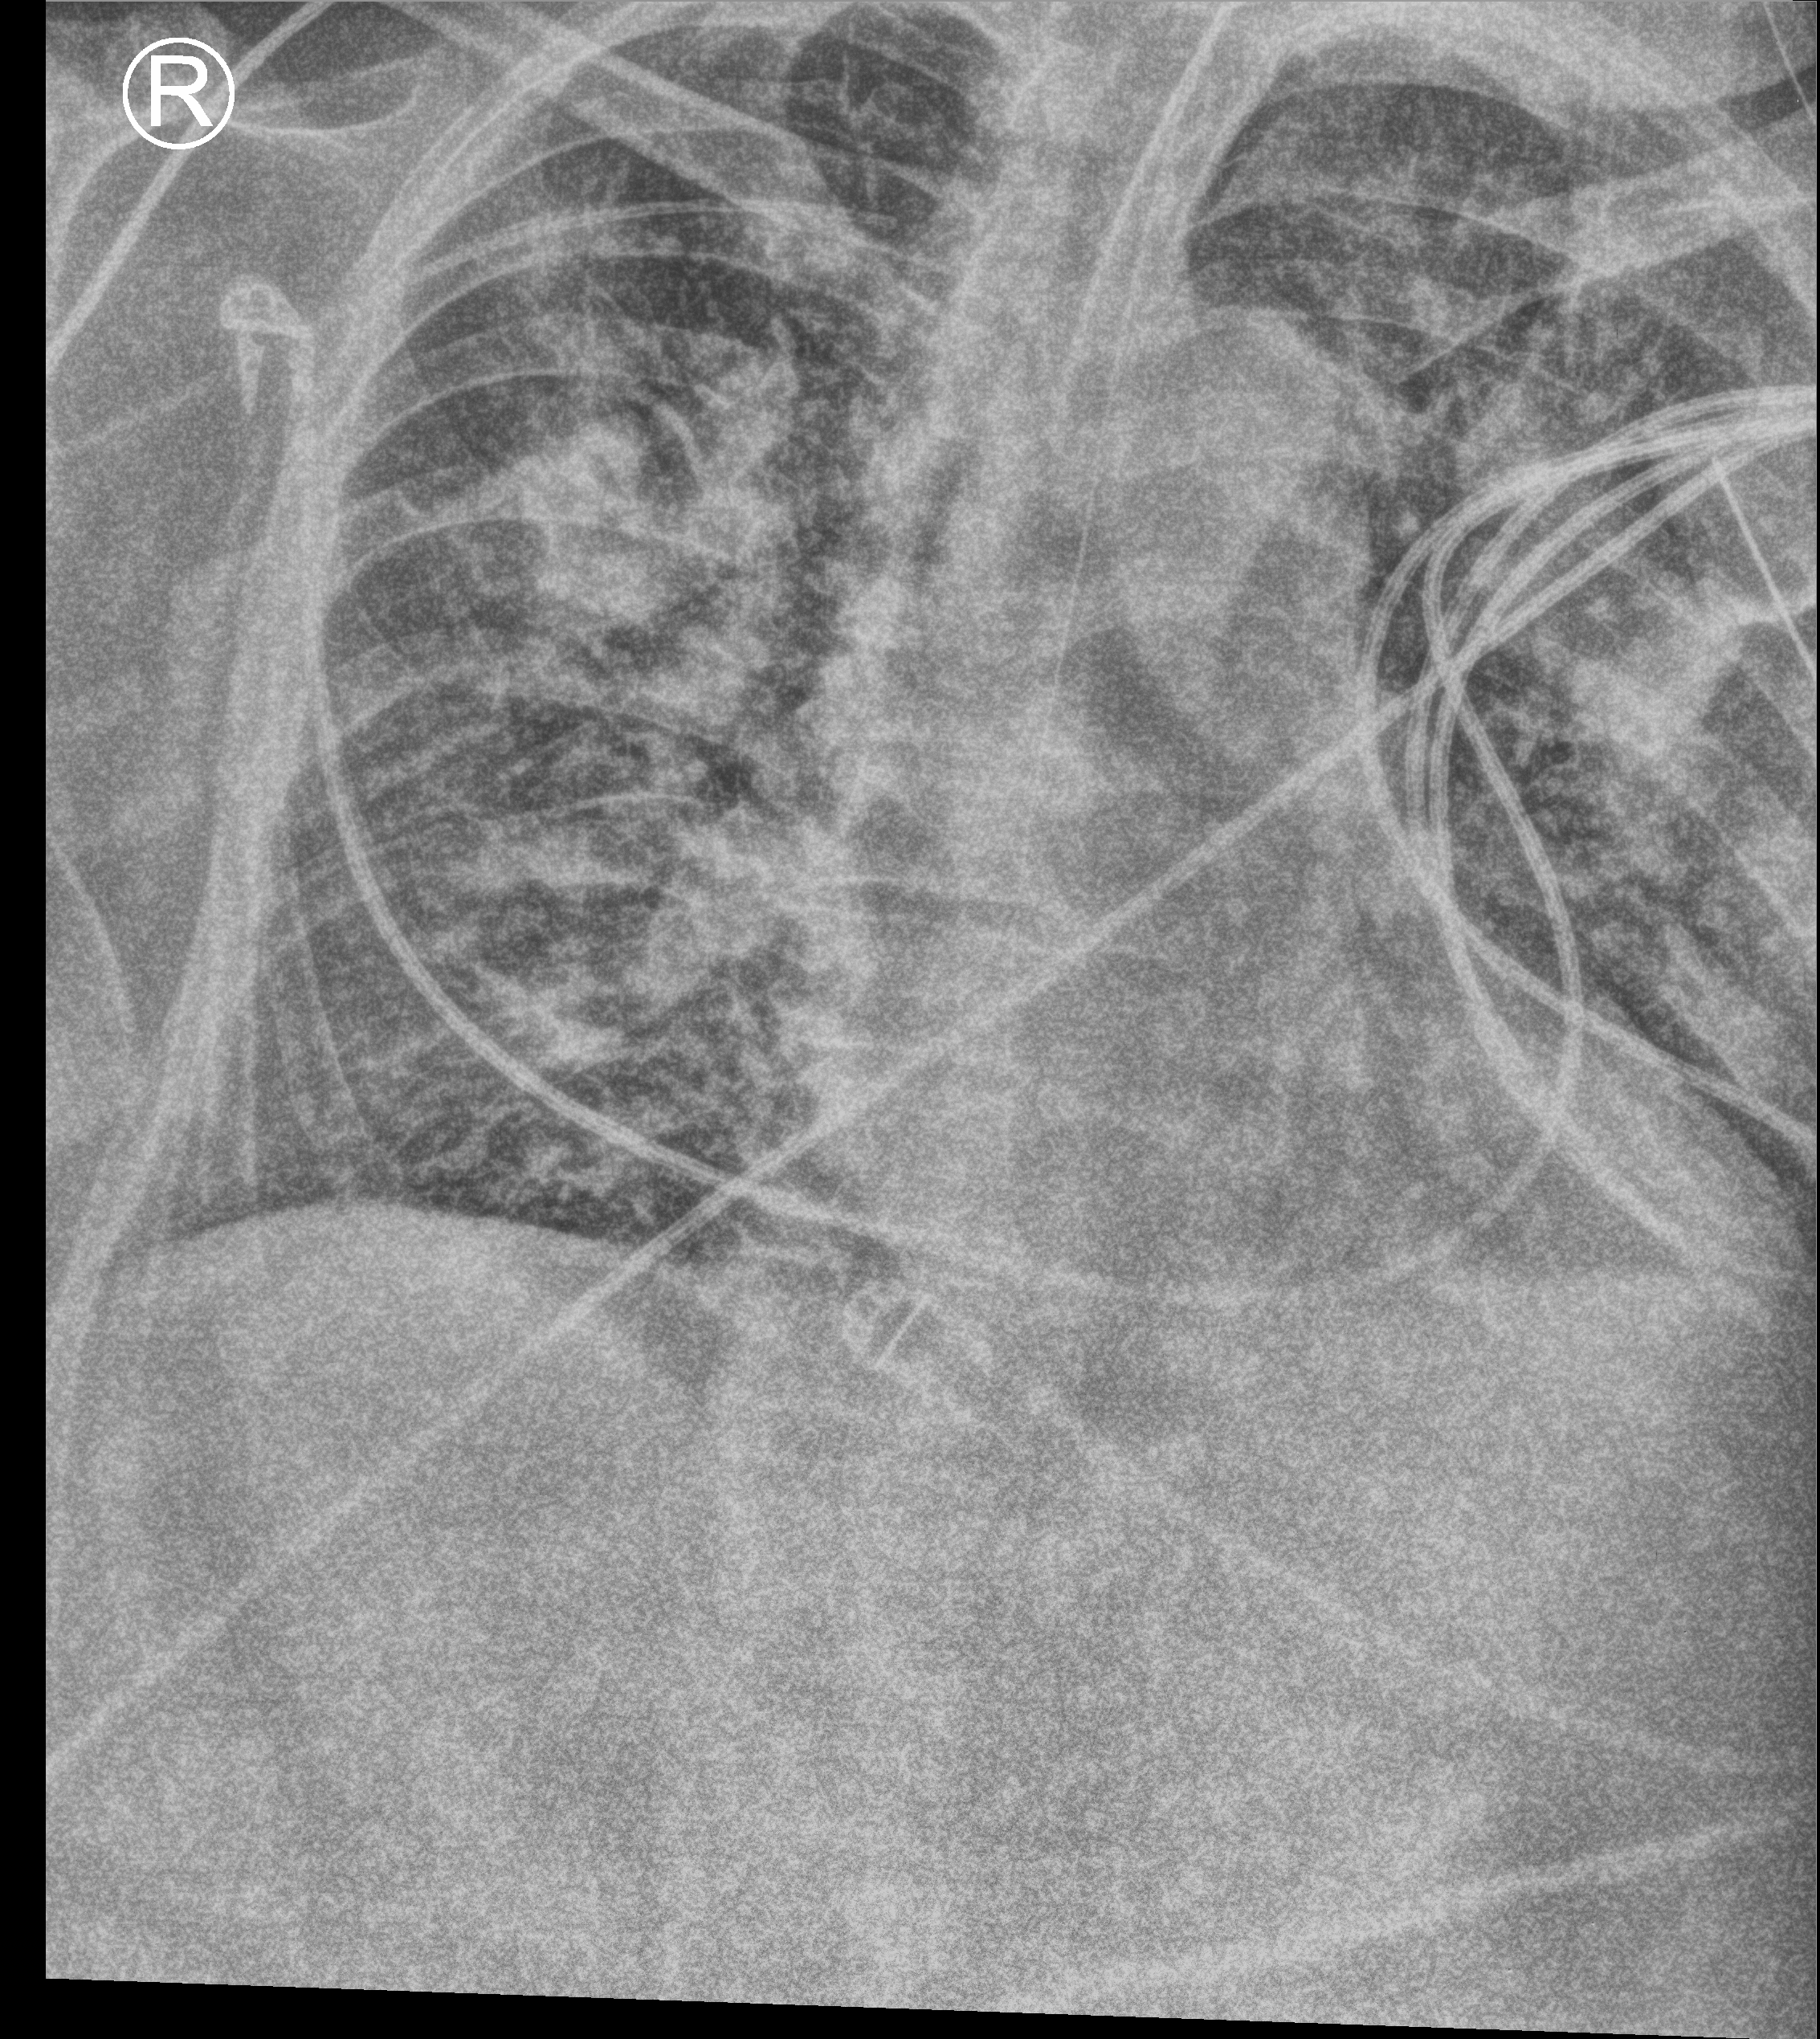
Portable chest radiograph, anteroposterior (AP) projection. Male patient hospitalised with COVID-19, age 60–74 years.
Hospital-stay facts (about this admission, not read from this image; timing relative to this image not recorded):
- hypertension (admission record): yes
- length of hospital stay: 20 days